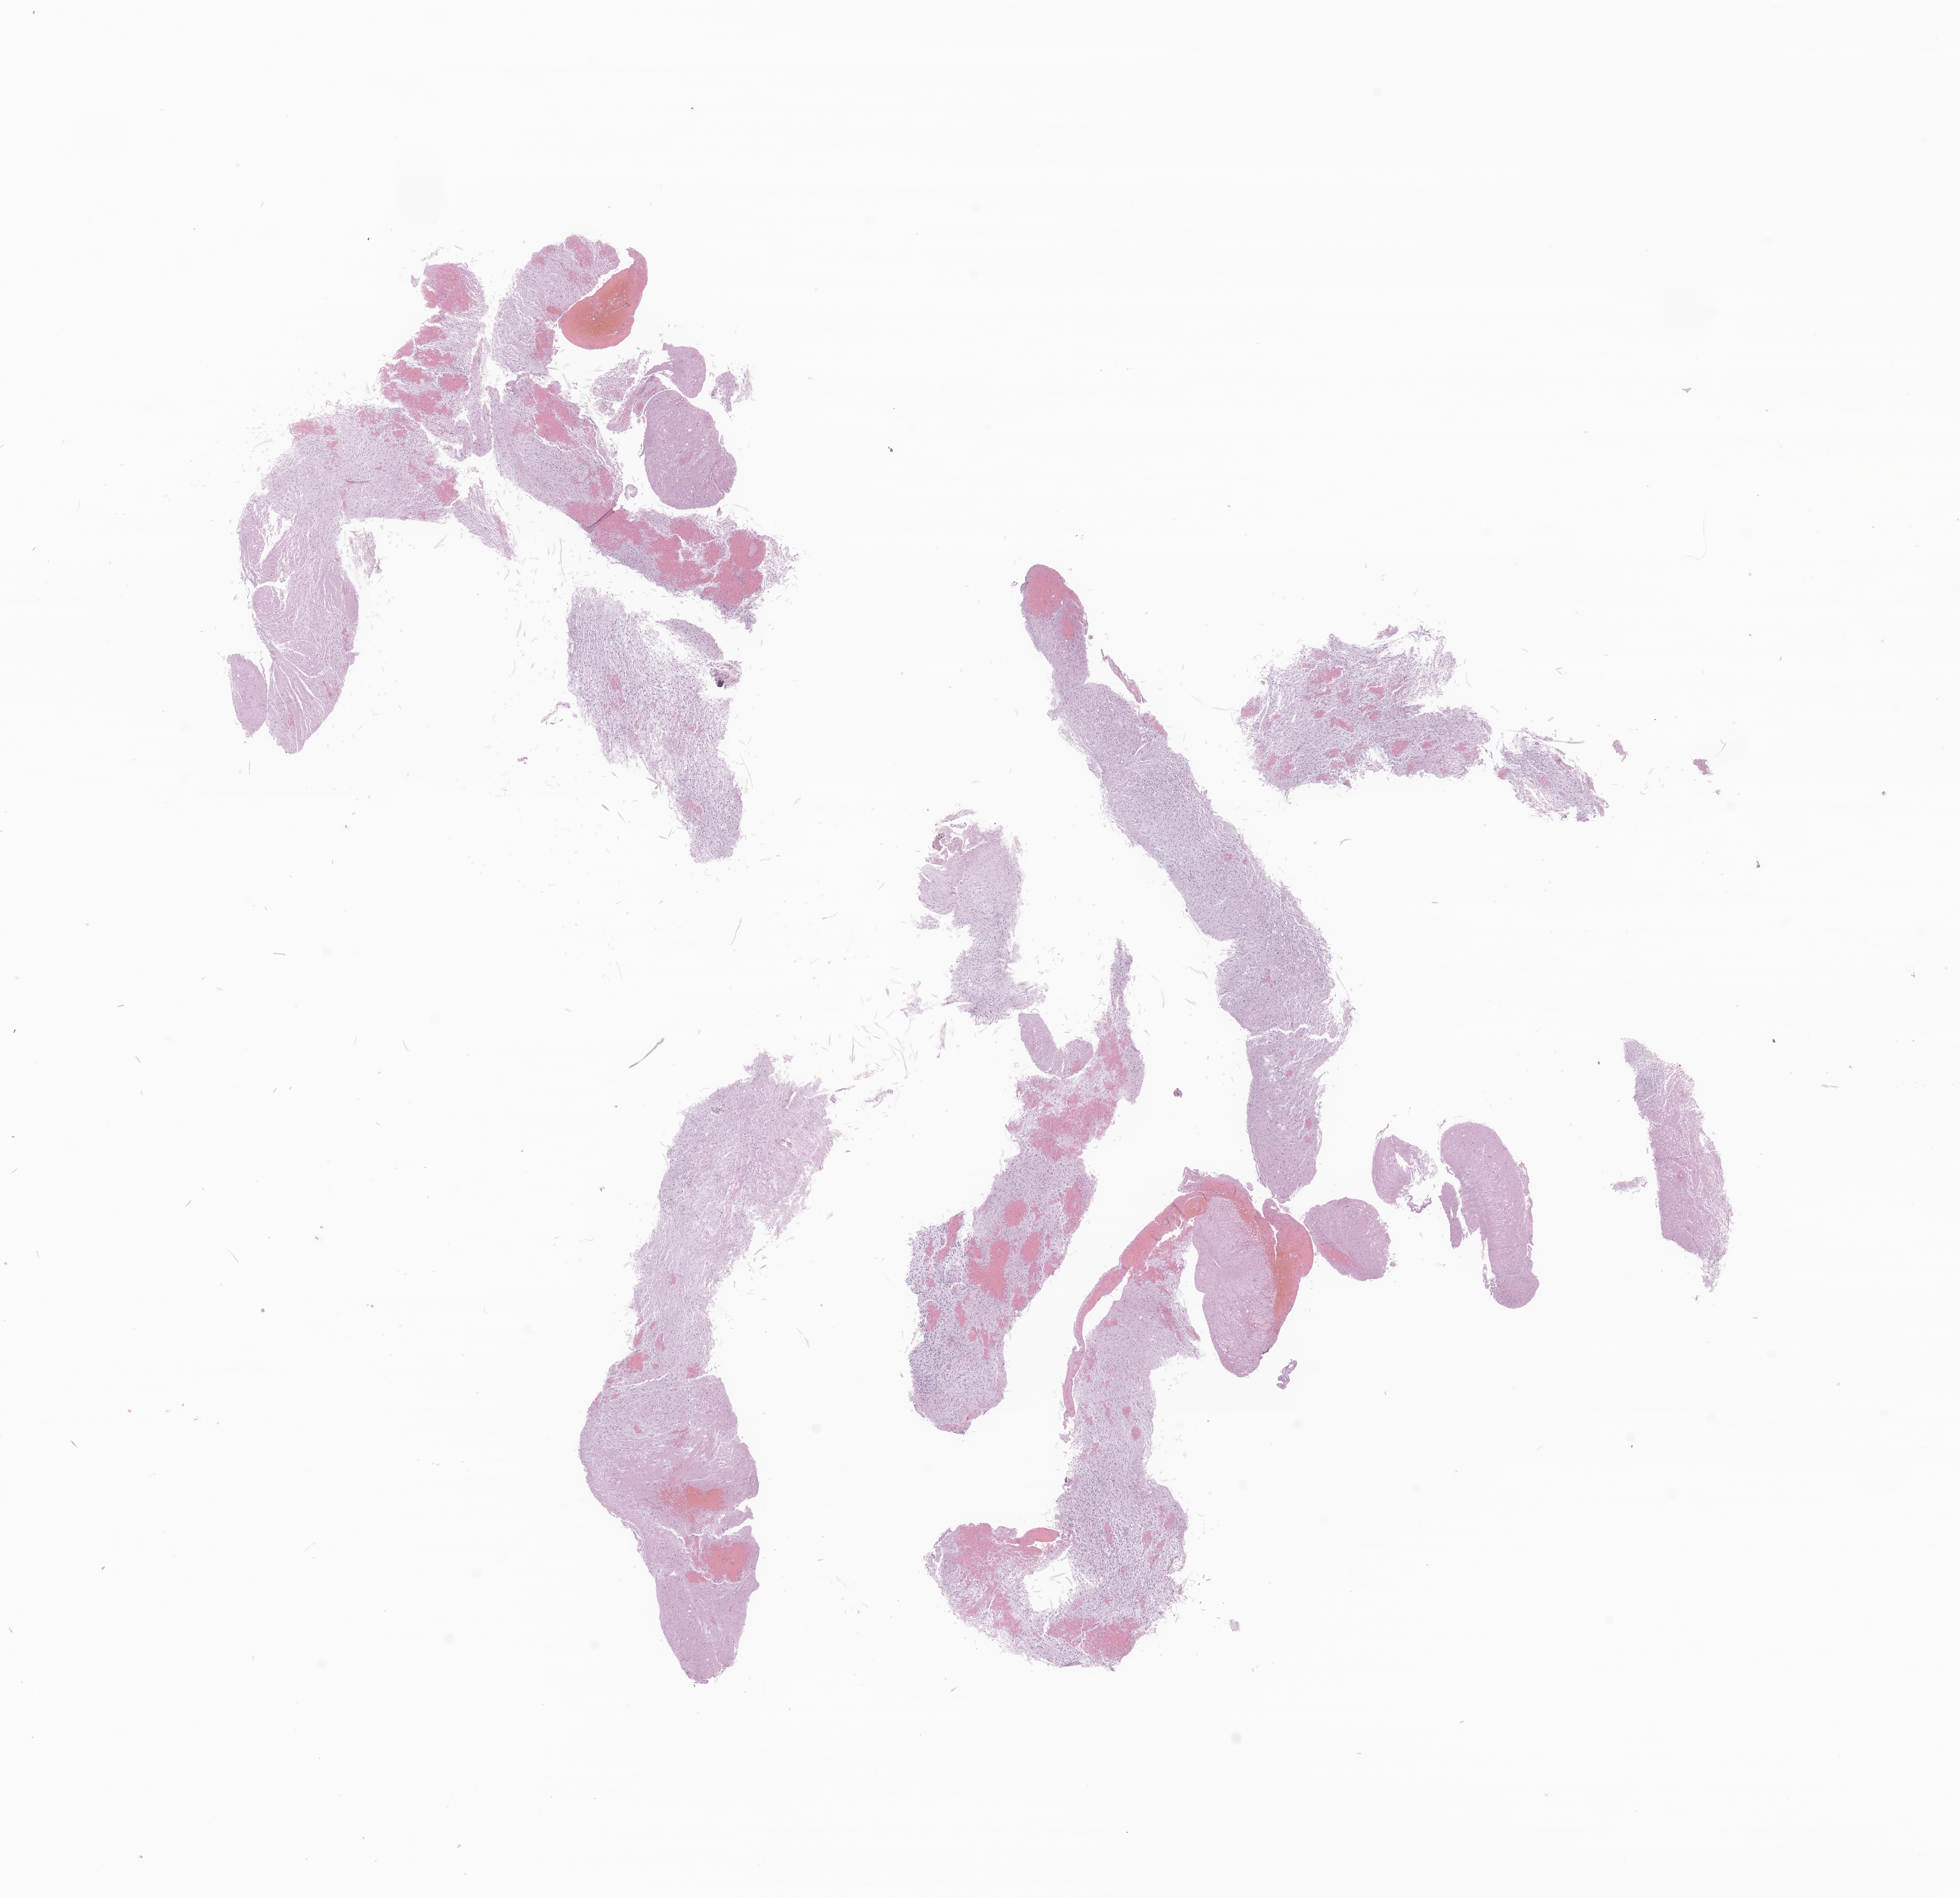
Whole-slide image, hematoxylin and eosin (H&E) stain of tumor tissue from the brain stem, a low-resolution overview of the entire scanned area, about 17.0 x 16.5 mm, formalin-fixed paraffin-embedded section. Patient female; age 59 months (4 years 11 months).
Recorded diagnosis: Glioma, malignant.